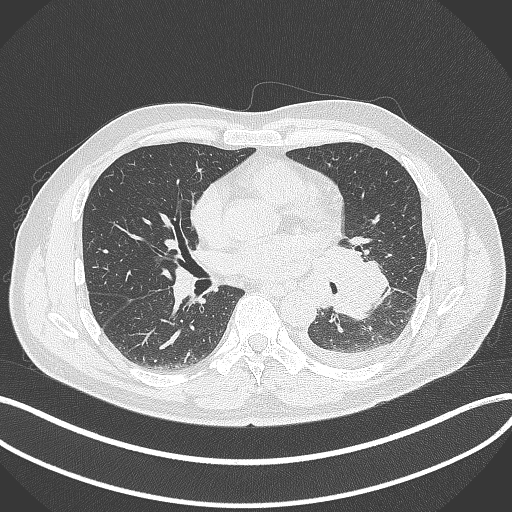
Chest CT, one axial slice. Position 178 of 342 along the scan axis. Reconstruction kernel B70f. Lung window (W 1500 / L -600 HU). 512 × 512 image matrix, field of view 400 × 400 mm. Male patient, age 58 years. From the clinical record (not read from this slice): clinical TNM (as recorded): T3 N1 M1b; histopathological grade: G3.
Outlined on this slice (rectangle marked by the reading radiologist):
- lung tumour (recorded histology: small cell carcinoma): bounding box (x1, y1, x2, y2) in pixels: (322, 242, 401, 325)